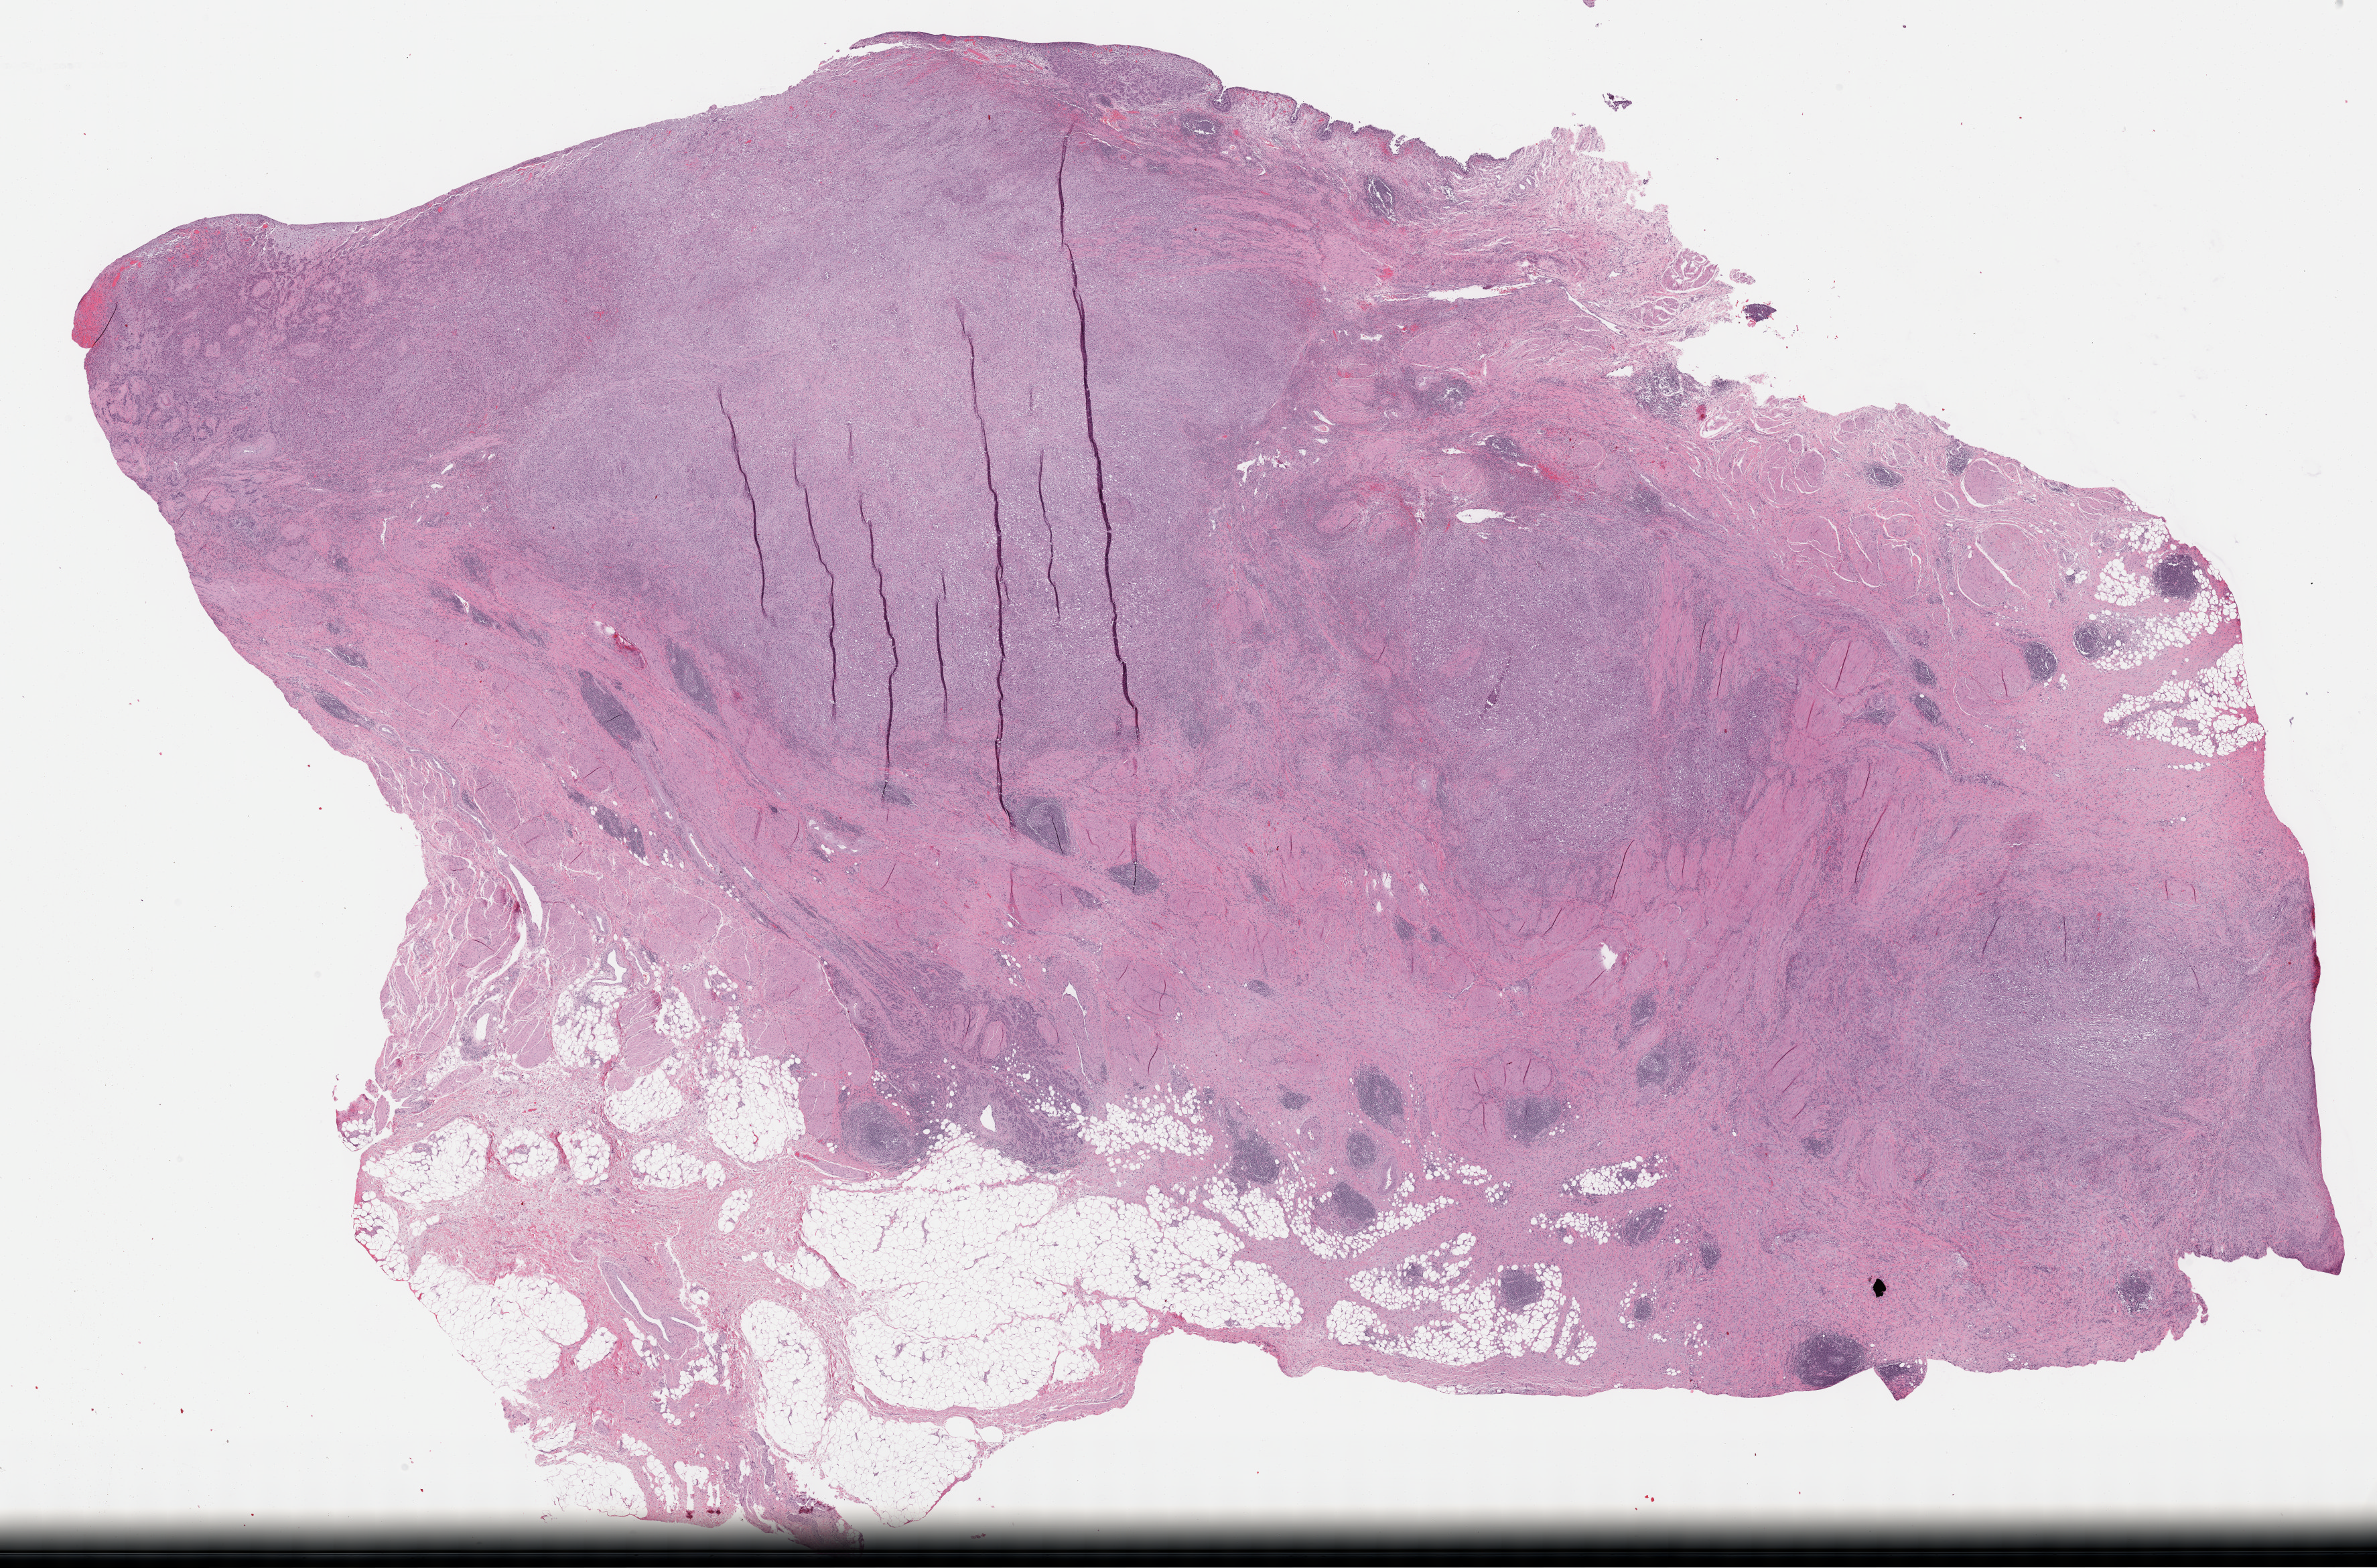
Digitized H&E-stained tissue section (whole slide), a low-resolution overview of the entire scanned area, about 28.7 x 18.9 mm (from a 40x scan). FFPE section. Sample: primary tumour, bladder. Patient: female, age at initial diagnosis 63 years. Histologic grade: high grade.
AJCC pathologic stage: IV (6th edition). Pathologic diagnosis: Transitional cell carcinoma.